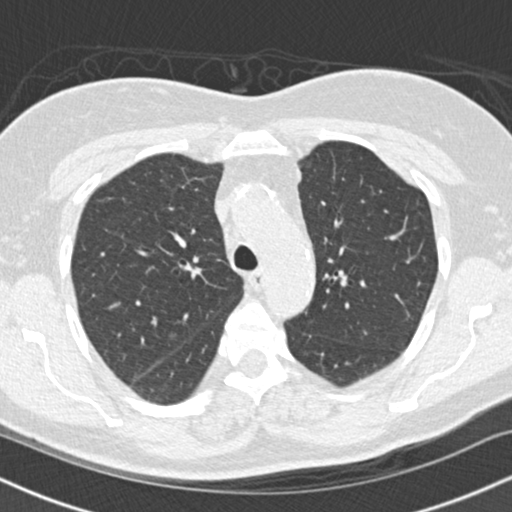
Axial slice from a low-dose chest CT screening exam. Baseline annual screen. Lung window (W 1500 / L -600 HU). 2 mm slice thickness. Slice 40 of 145 in the series. Female participant, aged 66 years at enrolment.
• Expert-annotated lung lesion, box from (x=156, y=322) to (x=187, y=354) px.
• Screening reader's record for this exam (one nodule recorded; not confirmed to be the boxed lesion): non-calcified nodule or mass ≥4 mm, right lower lobe, 10 × 8 mm, smooth margins, soft tissue attenuation.